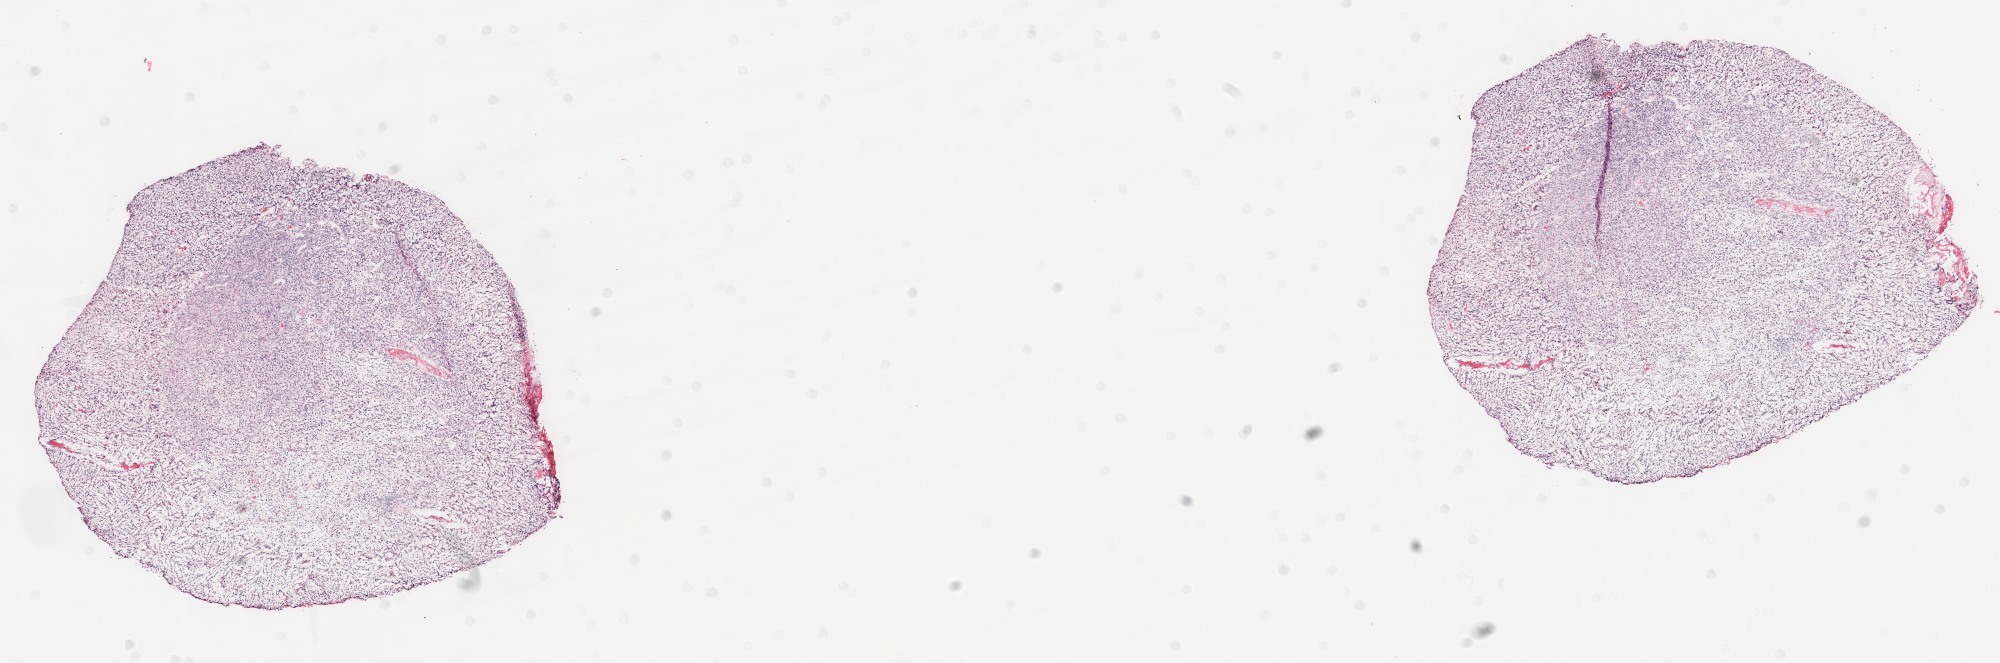
H&E-stained whole-slide image, low-resolution overview of the scanned area, about 16.0 x 5.3 mm, frozen section from the top of the tissue portion, sample: primary tumour, brain. Female patient; age at initial diagnosis 69 years. Composition of this section per pathologist review: tumour cells 90%, tumour nuclei 90%, normal cells 0%, stromal cells 10%, necrosis 0%.
• pathologic diagnosis: Glioblastoma